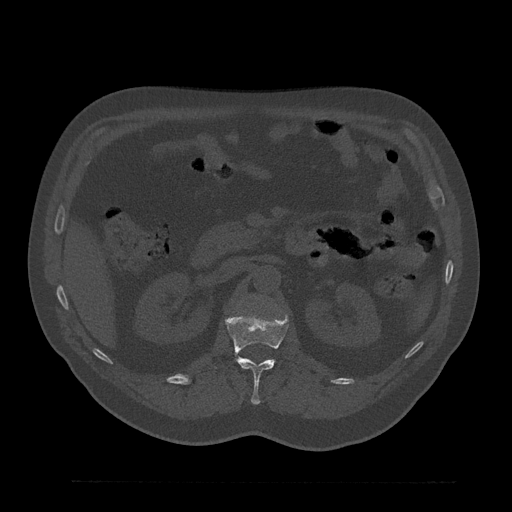
CT including the spine, one axial slice. Position 156 of 797 along the scan axis. Reconstruction kernel Br40s/3. 120 kVp. Bone window (W 1800 / L 400 HU). 512 × 512 image matrix, field of view 430 × 430 mm. Patient: male, 61 years. From the clinical record (not read from this slice): primary cancer: prostate.
Structures marked on this image (semi-automatic segmentation, software-assisted and operator-edited):
- L1 vertebra: bounding box [x1, y1, x2, y2] px = [211, 313, 288, 405]